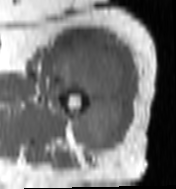
MRI of an extremity soft-tissue mass, one axial slice. Position 80 of 100 along the scan axis. MR volume resampled by the dataset authors to the PET/CT grid (not the native acquisition matrix). 3.27 mm slice thickness. 176 × 189 image matrix, field of view 172 × 185 mm. Female patient. From the clinical record (not read from this slice): histological type: undifferentiated – high grade; grade: high; site of the primary tumour: left thigh.
Structures marked on this image (expert contour drawn on MRI and transferred to this co-registered scan by the dataset authors):
- gross tumour volume including surrounding oedema: box from (x=51, y=45) to (x=125, y=152) px
- gross tumour volume (mass): (x=53, y=50)–(x=125, y=151)